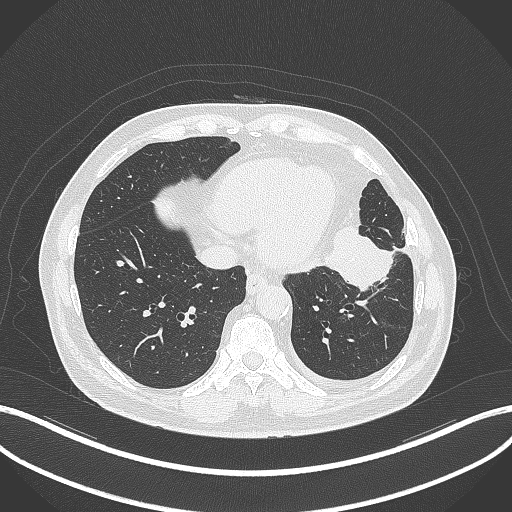
Chest CT, one axial slice; reconstruction kernel B70f; lung window (W 1500 / L -600 HU); 1 mm slice thickness; 512 × 512 image matrix, field of view 400 × 400 mm. Male patient, age 68 years. From the clinical record (not read from this slice): clinical TNM (as recorded): T2b N0 M0.
Outlined on this slice (bounding box drawn by a radiologist):
- lung tumour (recorded histology: squamous cell carcinoma): box from (x=323, y=225) to (x=396, y=296) px